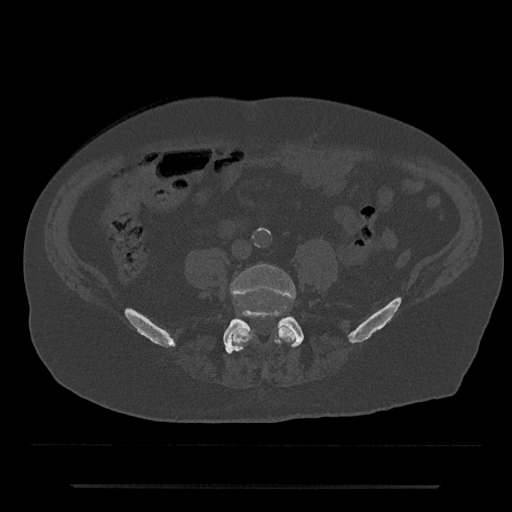
CT including the spine, one axial slice; position 317 of 797 along the scan axis; reconstruction kernel Br40s/3; 120 kVp; bone window (W 1800 / L 400 HU); 0.5 mm slice thickness; 512 × 512 image matrix, field of view 434 × 434 mm. Male patient, age 80 years. From the clinical record (not read from this slice): primary cancer: prostate.
Outlined on this slice (semi-automatically segmented with operator editing):
- L4 vertebra: box from (x=230, y=264) to (x=296, y=349) px
- L5 vertebra: (x=223, y=311)–(x=304, y=354)